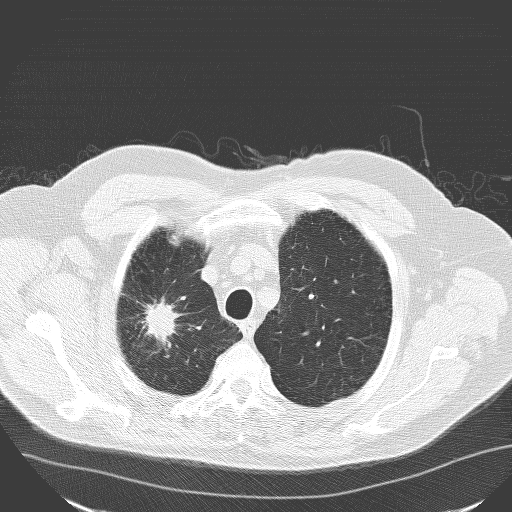
Axial slice from a low-dose chest CT screening exam. Baseline screening round. Lung window (W 1500 / L -600 HU). Lung (sharp) reconstruction kernel (D). 120 kVp. Male participant, aged 71 years at enrolment. Current smoker at enrolment.
• Expert reader's lesion annotation, bounding box (x1, y1, x2, y2) in pixels: (116, 281, 189, 357).
• Reader record for this screening exam (exam-level; its link to the box is not recorded): non-calcified nodule or mass ≥4 mm, right upper lobe, 30 × 25 mm, spiculated (stellate) margins, soft tissue attenuation.
• Official screen result: positive, change unspecified: nodule(s) >= 4 mm or enlarging nodule(s), mass(es), or other non-specific abnormalities suspicious for lung cancer.
• Later outcome: lung cancer diagnosed 182 days after this screen — squamous cell carcinoma, NOS, right upper lobe, poorly differentiated (G3), stage IA (AJCC 6th edition), 30 mm at pathology.